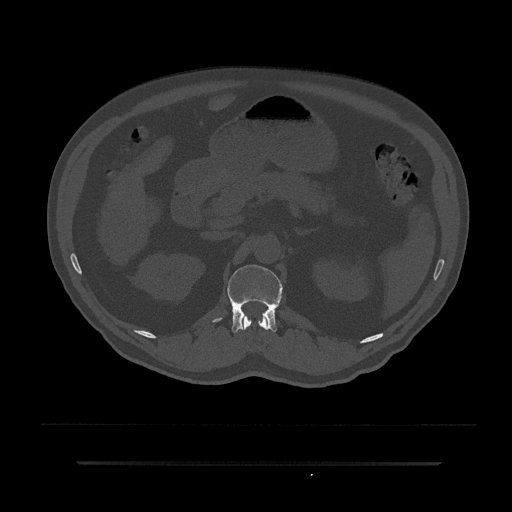
CT including the spine, one axial slice; slice 167 of 797 in the series (ordered by position); 120 kVp; bone window (W 1800 / L 400 HU); 0.5 mm slice thickness; 512 × 512 image matrix, field of view 464 × 464 mm. Male patient, age 59 years. Case-level facts recorded for this patient, not image findings: primary cancer: bile ducts.
Outlined on this slice (semi-automatic segmentation, software-assisted and operator-edited):
- L1 vertebra: bounding box [x1, y1, x2, y2] px = [213, 265, 283, 334]
- T12 vertebra: [241, 316, 268, 330]